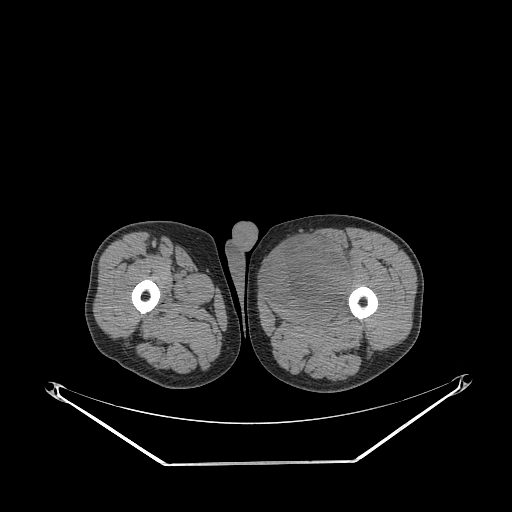
CT of an extremity soft-tissue mass (from a PET/CT study), one axial slice. Position 251 of 267 along the scan axis. Reconstruction kernel STANDARD. 140 kVp. Soft-tissue window (W 400 / L 40 HU). 512 × 512 image matrix, field of view 500 × 500 mm. Male patient. From the clinical record (not read from this slice): histological type: pleiomorphic liposarcoma; grade: high; site of the primary tumour: left thigh.
Structures marked on this image (expert contour drawn on MRI and transferred to this co-registered scan by the dataset authors):
- gross tumour volume including surrounding oedema: bounding box <265,235,353,314> (left, top, right, bottom; pixels)
- gross tumour volume (mass): <265,235,350,314>